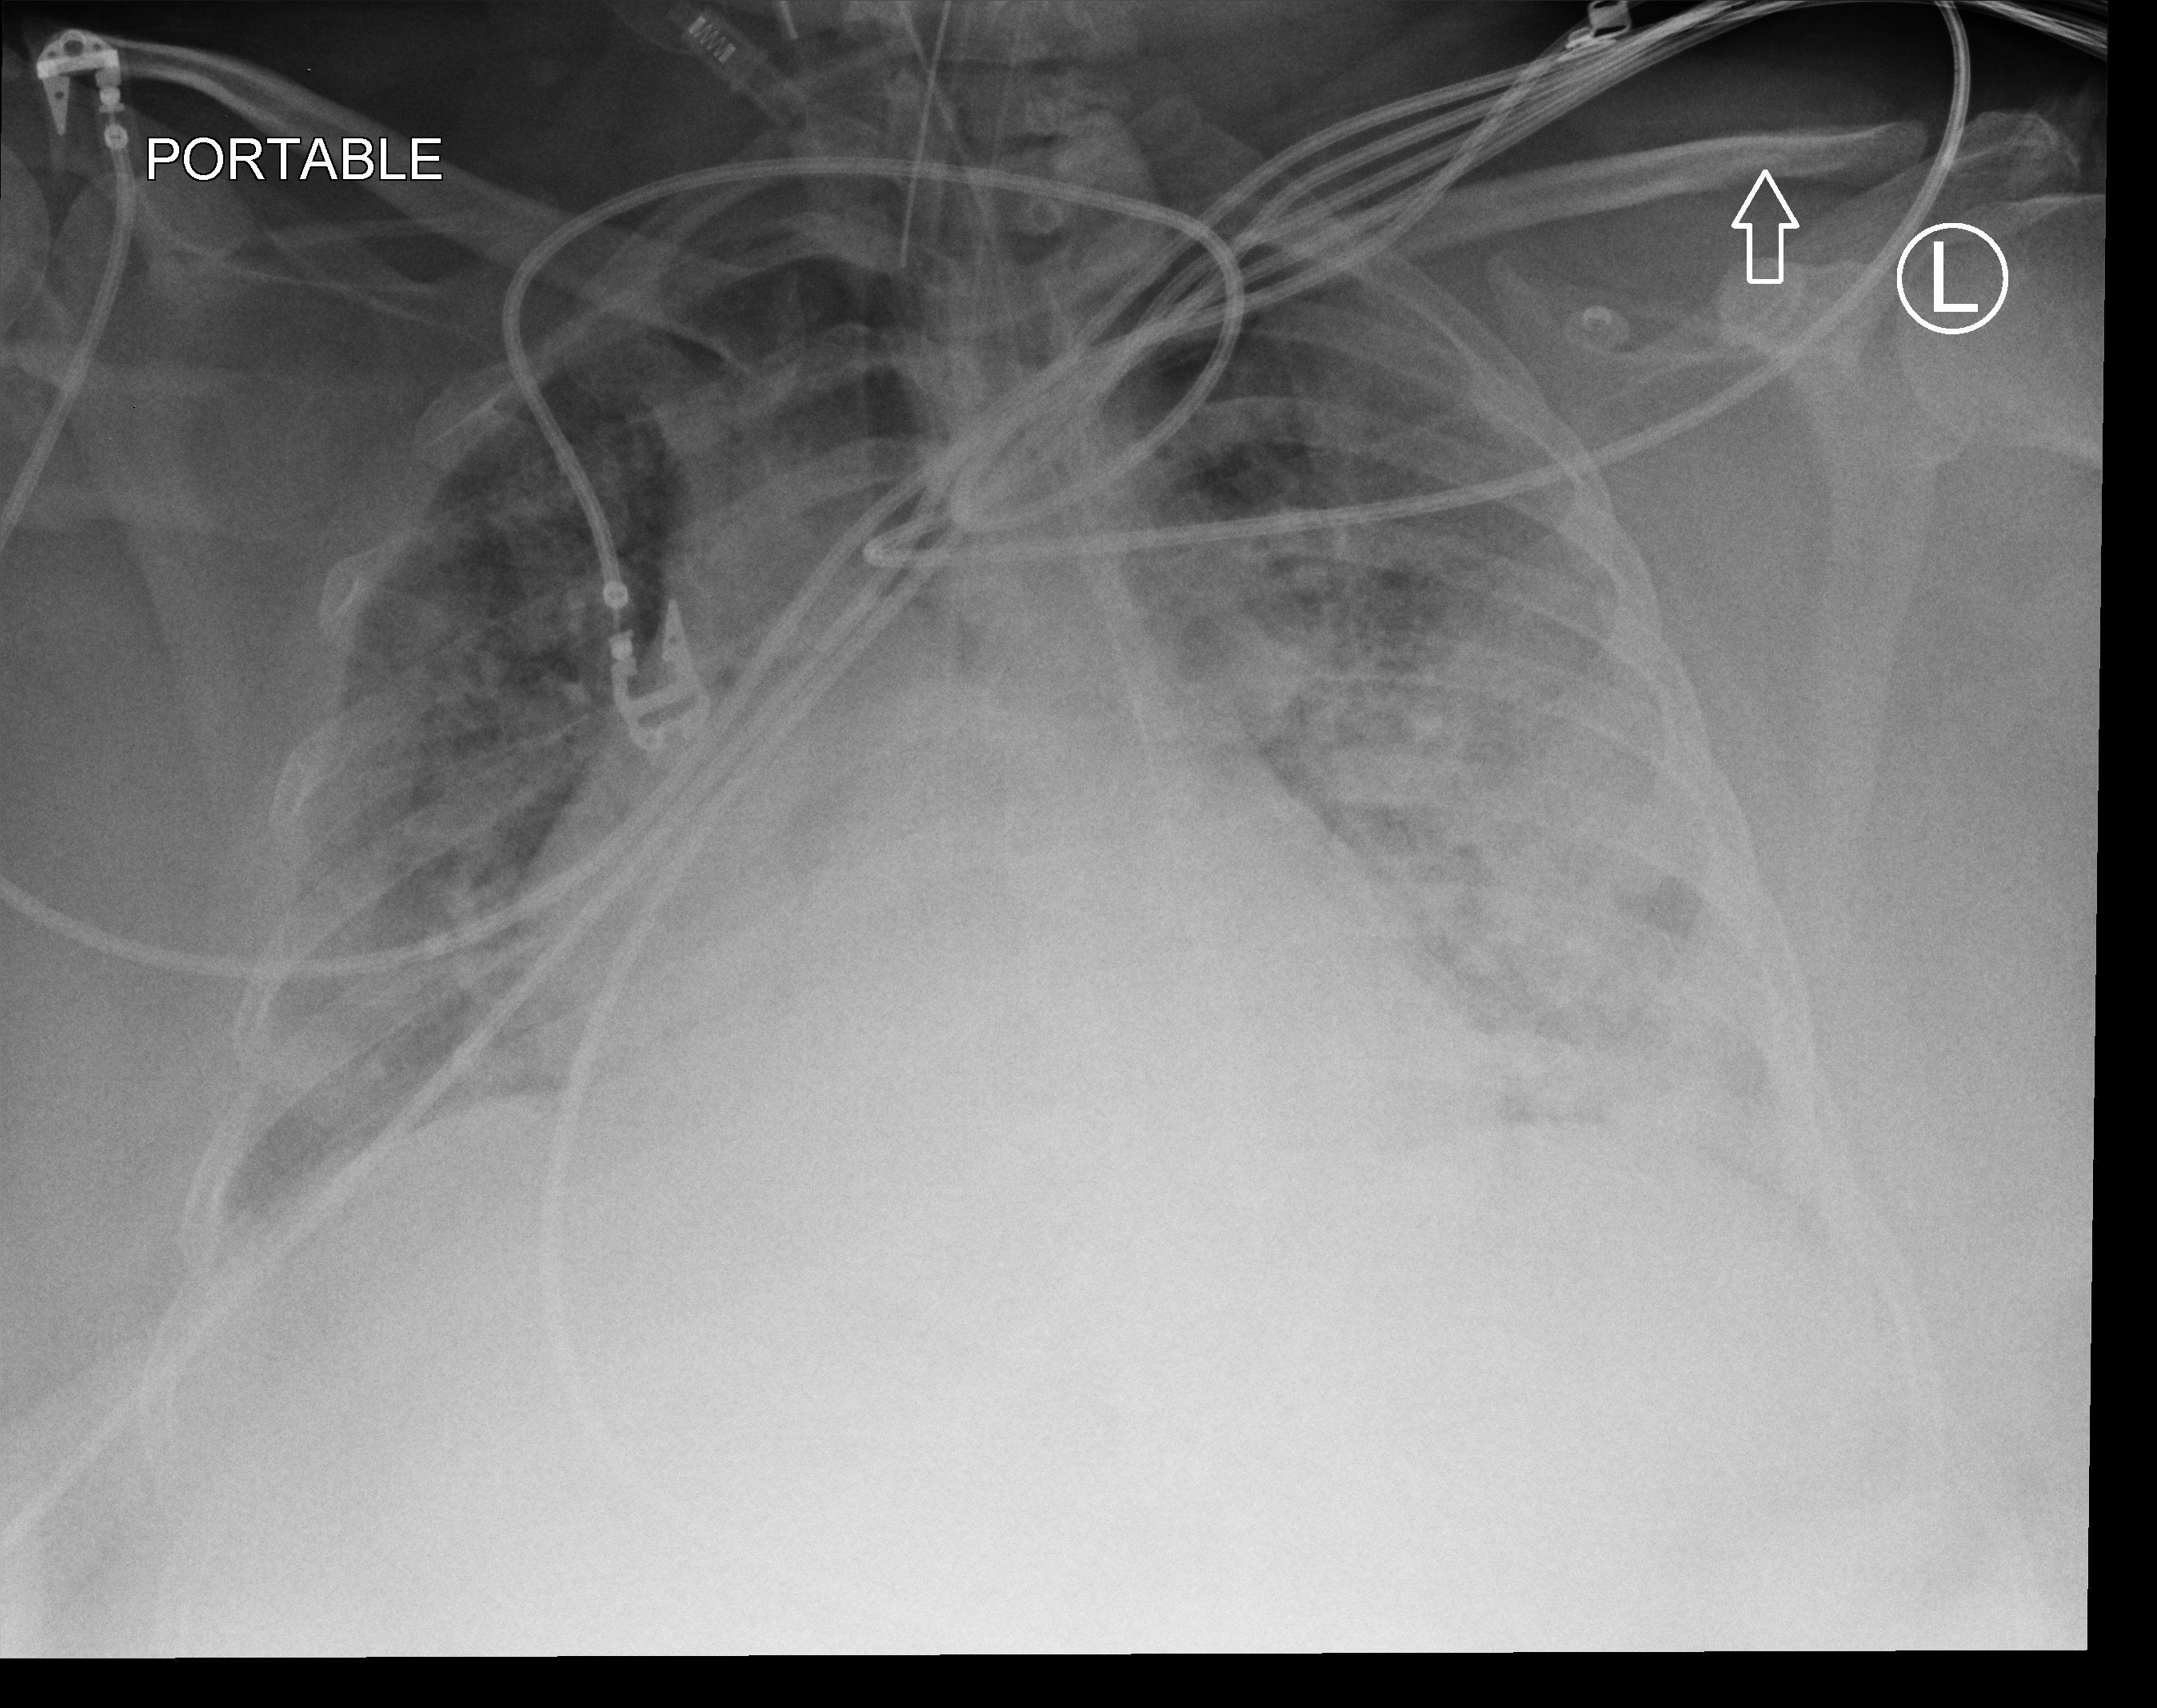
Chest X-ray (portable), anteroposterior (AP) projection. Female patient hospitalised with COVID-19, age 18–59 years.
Hospital-stay facts (about this admission, not read from this image; timing relative to this image not recorded): mechanically ventilated during this hospital stay: yes.